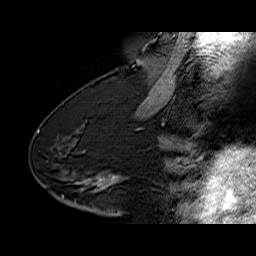
Breast MRI (dynamic contrast-enhanced), one sagittal slice. Slice 34 of 60 in the series (ordered by position). Dynamic contrast-enhanced series, time point 2 of 6 at this slice position (early post-contrast). 1.5 T. TE 6.4 ms, TR 32.9 ms. 4 mm slice thickness. 256 × 256 image matrix, field of view 200 × 200 mm. Female patient. Case-level facts recorded for this patient, not image findings: setting: breast cancer imaged before/during neoadjuvant chemotherapy; receptor status: HR-positive, HER2-negative.
Outlined on this slice (semi-automatically segmented with operator editing):
- analysis volume of interest (the breast-tissue region the enhancement analysis was run in; not a lesion): box from (x=68, y=163) to (x=128, y=203) px
- tumour enhancement mask (voxels above the 100 % enhancement threshold inside the analysis volume of interest): (x=97, y=175)–(x=119, y=190)